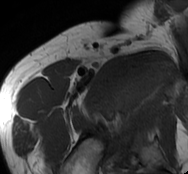
MRI of an extremity soft-tissue mass, one axial slice. Slice 71 of 93 in the series (ordered by position). MR volume resampled by the dataset authors to the PET/CT grid (not the native acquisition matrix). 3.27 mm slice thickness. 188 × 174 image matrix, field of view 184 × 170 mm. Male patient. From the clinical record (not read from this slice): histological type: undifferentiated - pleiomorphic; grade: high; site of the primary tumour: right thigh.
Outlined on this slice (expert contour drawn on MRI and transferred to this co-registered scan by the dataset authors):
- gross tumour volume including surrounding oedema: box from (x=113, y=55) to (x=176, y=121) px
- gross tumour volume (mass): (x=113, y=62)–(x=171, y=116)